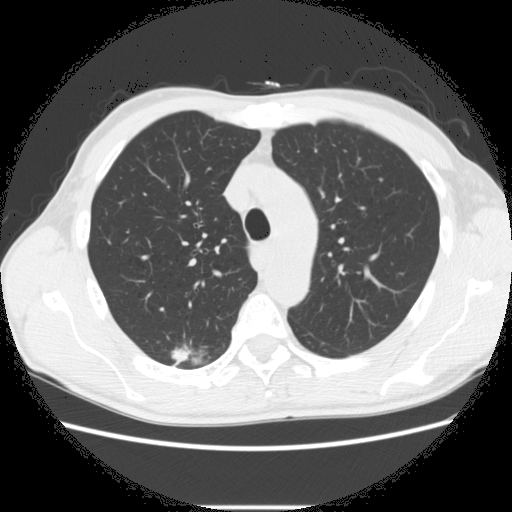
Chest CT (low-dose screening protocol), one axial image; second annual screen; lung window (W 1500 / L -600 HU); 2.5 mm slice thickness; standard (soft-tissue) reconstruction kernel (STANDARD); 512 × 512 image matrix, field of view 360 × 360 mm. Male participant, aged 66 years at enrolment.
Expert reader's lesion annotation, bounding box [x1, y1, x2, y2] px = [161, 337, 222, 374]. The screening reader recorded 5 non-calcified nodules or masses ≥4 mm on this exam (right lower lobe, right upper lobe, right upper lobe, right upper lobe, left lower lobe); which of them this box marks is not recorded. Official screen result: positive, change unspecified: nodule(s) >= 4 mm or enlarging nodule(s), mass(es), or other non-specific abnormalities suspicious for lung cancer. Lung cancer was diagnosed 75 days after this screen: adenocarcinoma, NOS, right upper lobe, undifferentiated (G4), stage IA (AJCC 6th edition), 20 mm at pathology.